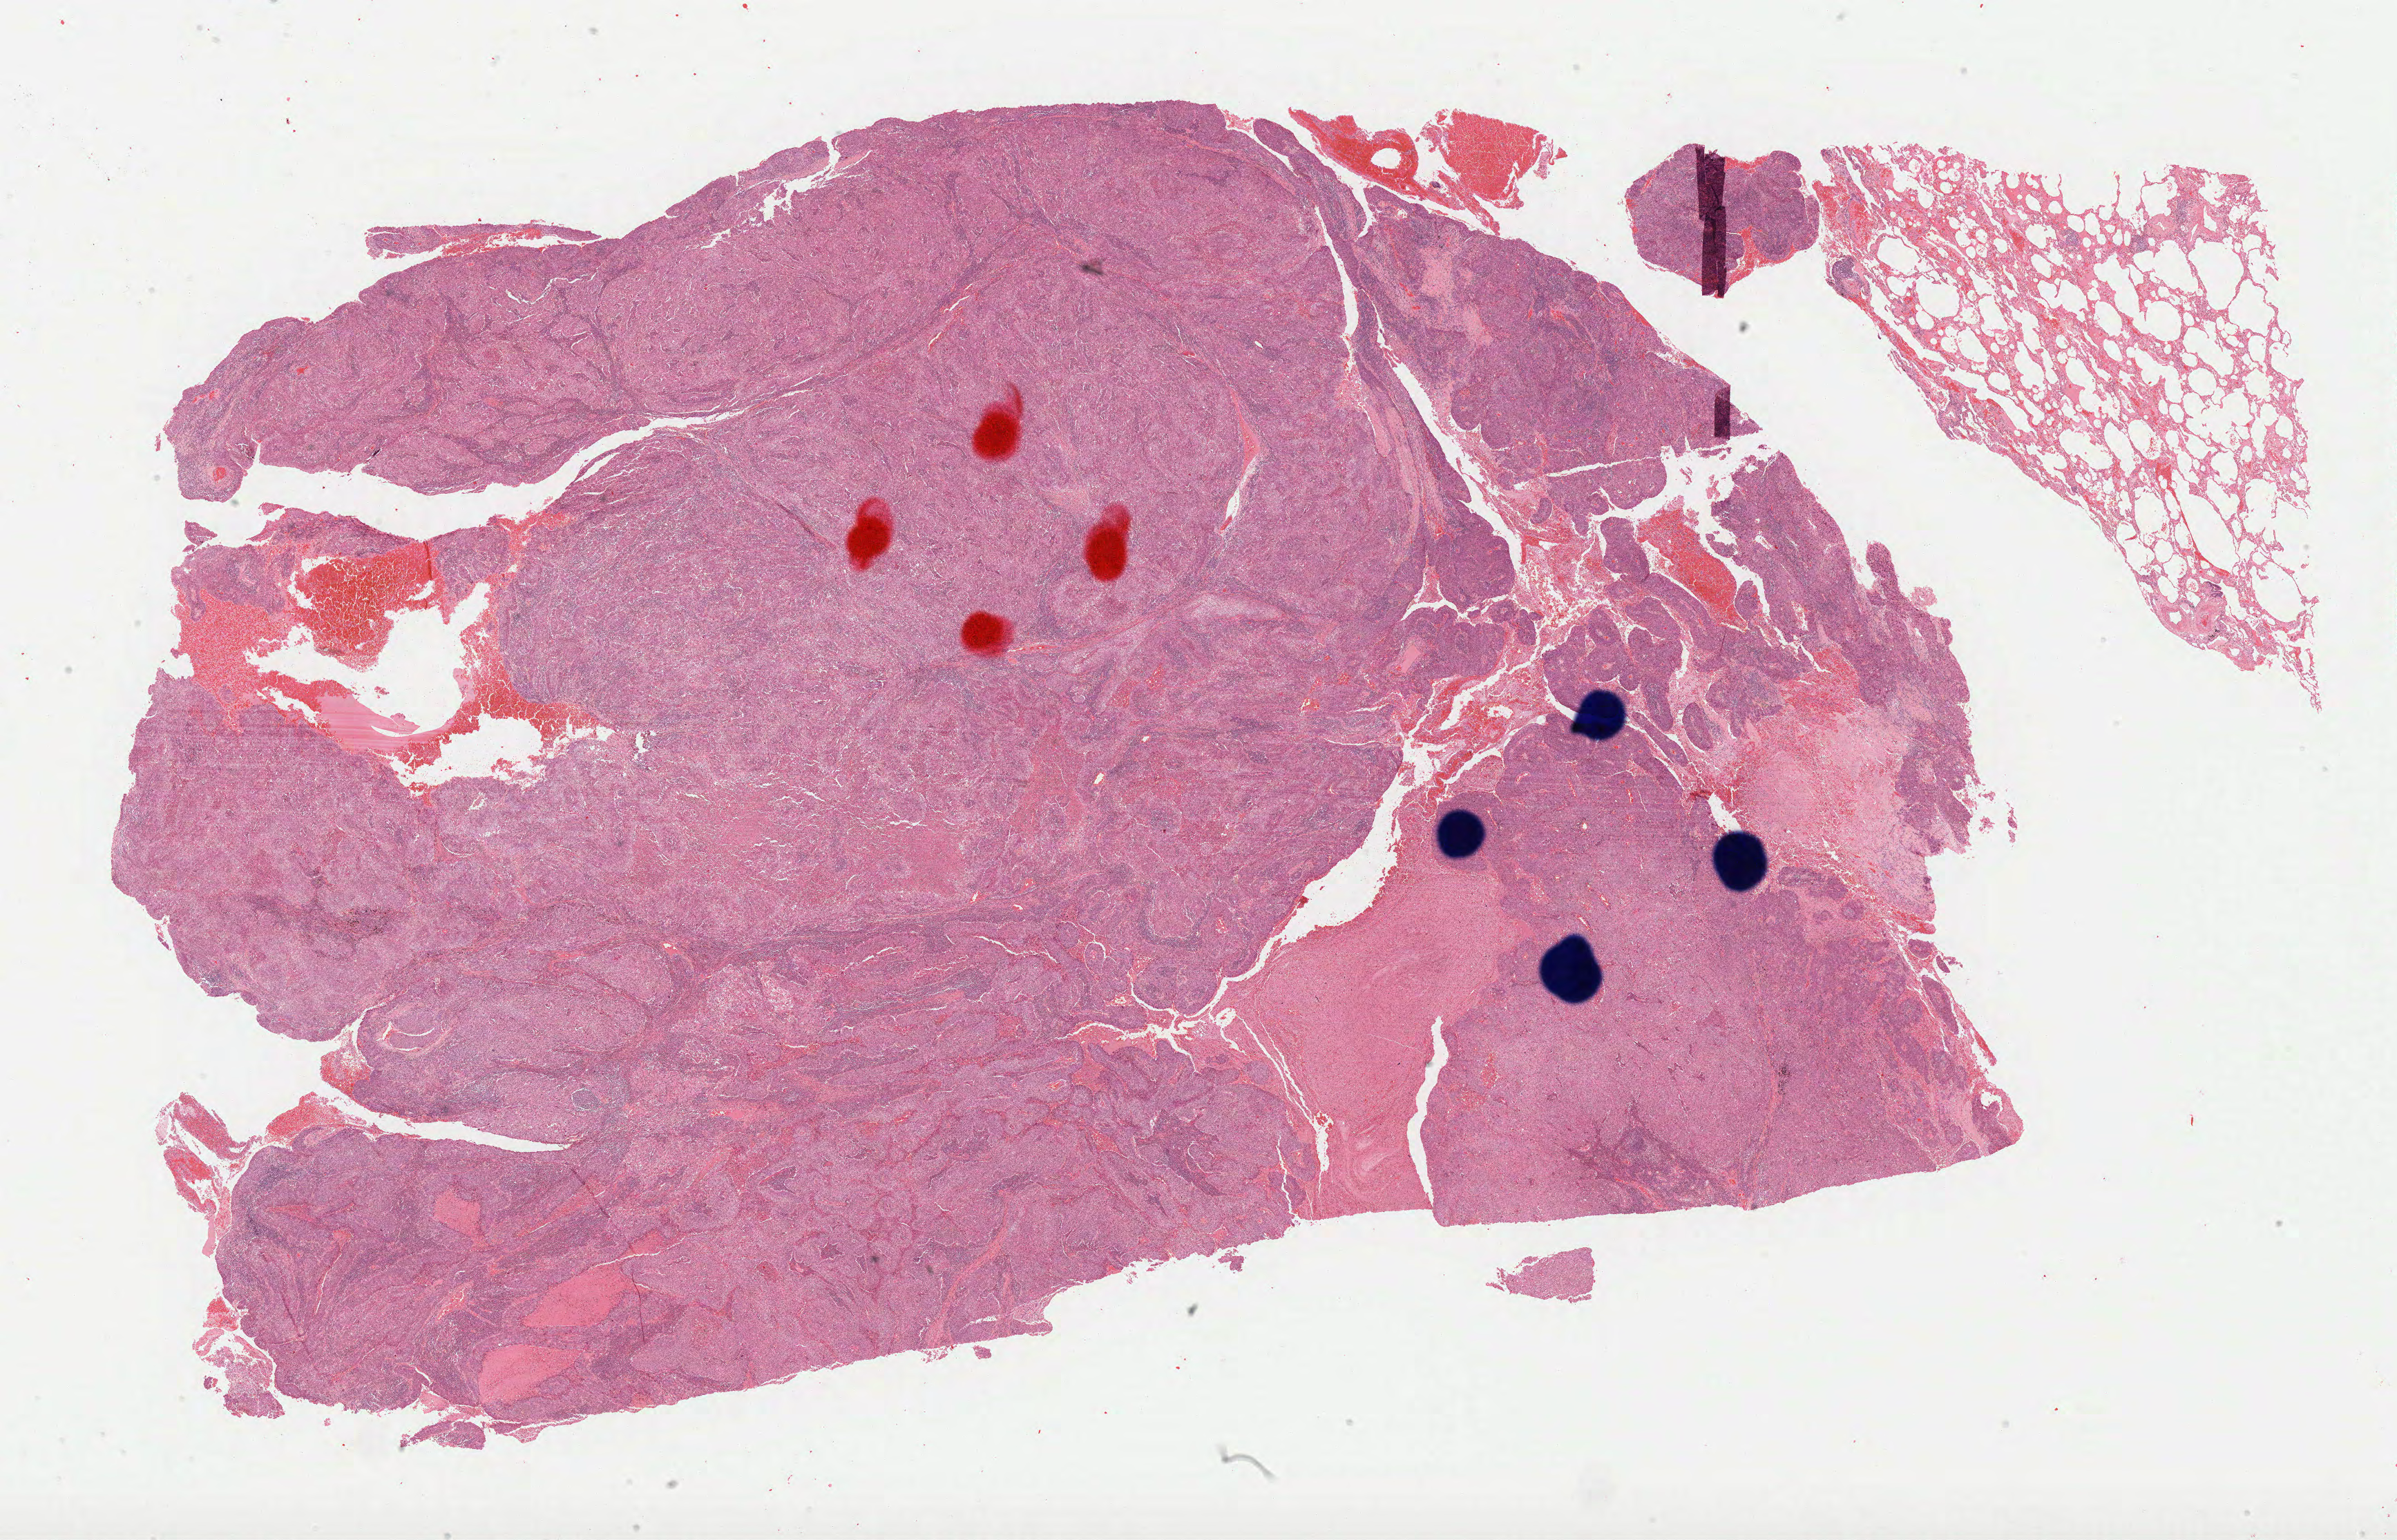
Whole-slide histology image, H&E — low-resolution overview of the scanned area, about 28.0 x 18.0 mm (slide scanned at 40x); formalin-fixed paraffin-embedded (FFPE) diagnostic section; lung, primary tumour sample. Patient: male, age at initial diagnosis 73 years.
Histologic diagnosis: Squamous cell carcinoma, NOS (lower lobe, lung).